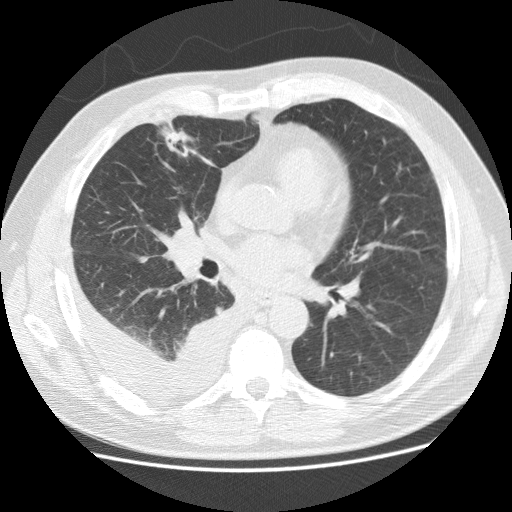
Axial slice from a low-dose chest CT screening exam, baseline screening round, lung window (W 1500 / L -600 HU), 120 kVp, slice 79 of 142 in the series, 512 × 512 image matrix, field of view 380 × 380 mm. Male participant, aged 65 years at enrolment. Current smoker at enrolment.
Expert-annotated lung lesion, bounding box (x1, y1, x2, y2) in pixels: (149, 121, 215, 173). Reader record for this screening exam (exam-level; its link to the box is not recorded): non-calcified nodule or mass ≥4 mm, right middle lobe, 22 × 15 mm, spiculated (stellate) margins, mixed attenuation. Official screen result: positive, change unspecified: nodule(s) >= 4 mm or enlarging nodule(s), mass(es), or other non-specific abnormalities suspicious for lung cancer. Later outcome: lung cancer diagnosed 4 days after this screen — adenocarcinoma, NOS, right middle lobe, stage IV (AJCC 6th edition), 20 mm at pathology.